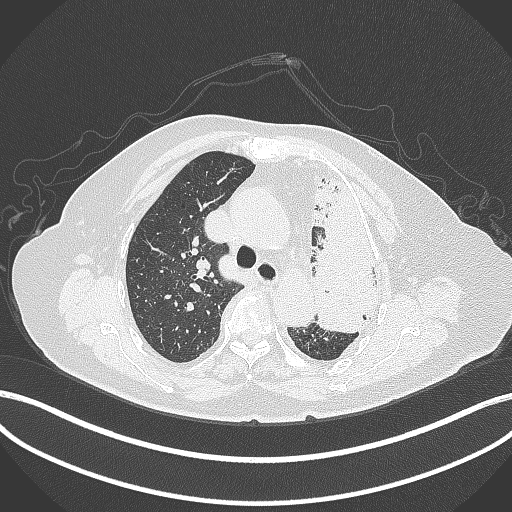
Chest CT, one axial slice. Slice 281 of 399 in the series (ordered by position). Lung window (W 1500 / L -600 HU). 1 mm slice thickness. 512 × 512 image matrix. Female patient, age 75 years. From the clinical record (not read from this slice): clinical TNM (as recorded): T3 N3 M1.
Annotated regions visible in this slice (rectangle marked by the reading radiologist):
- lung tumour (recorded histology: adenocarcinoma): bounding box [x1, y1, x2, y2] px = [306, 165, 383, 335]